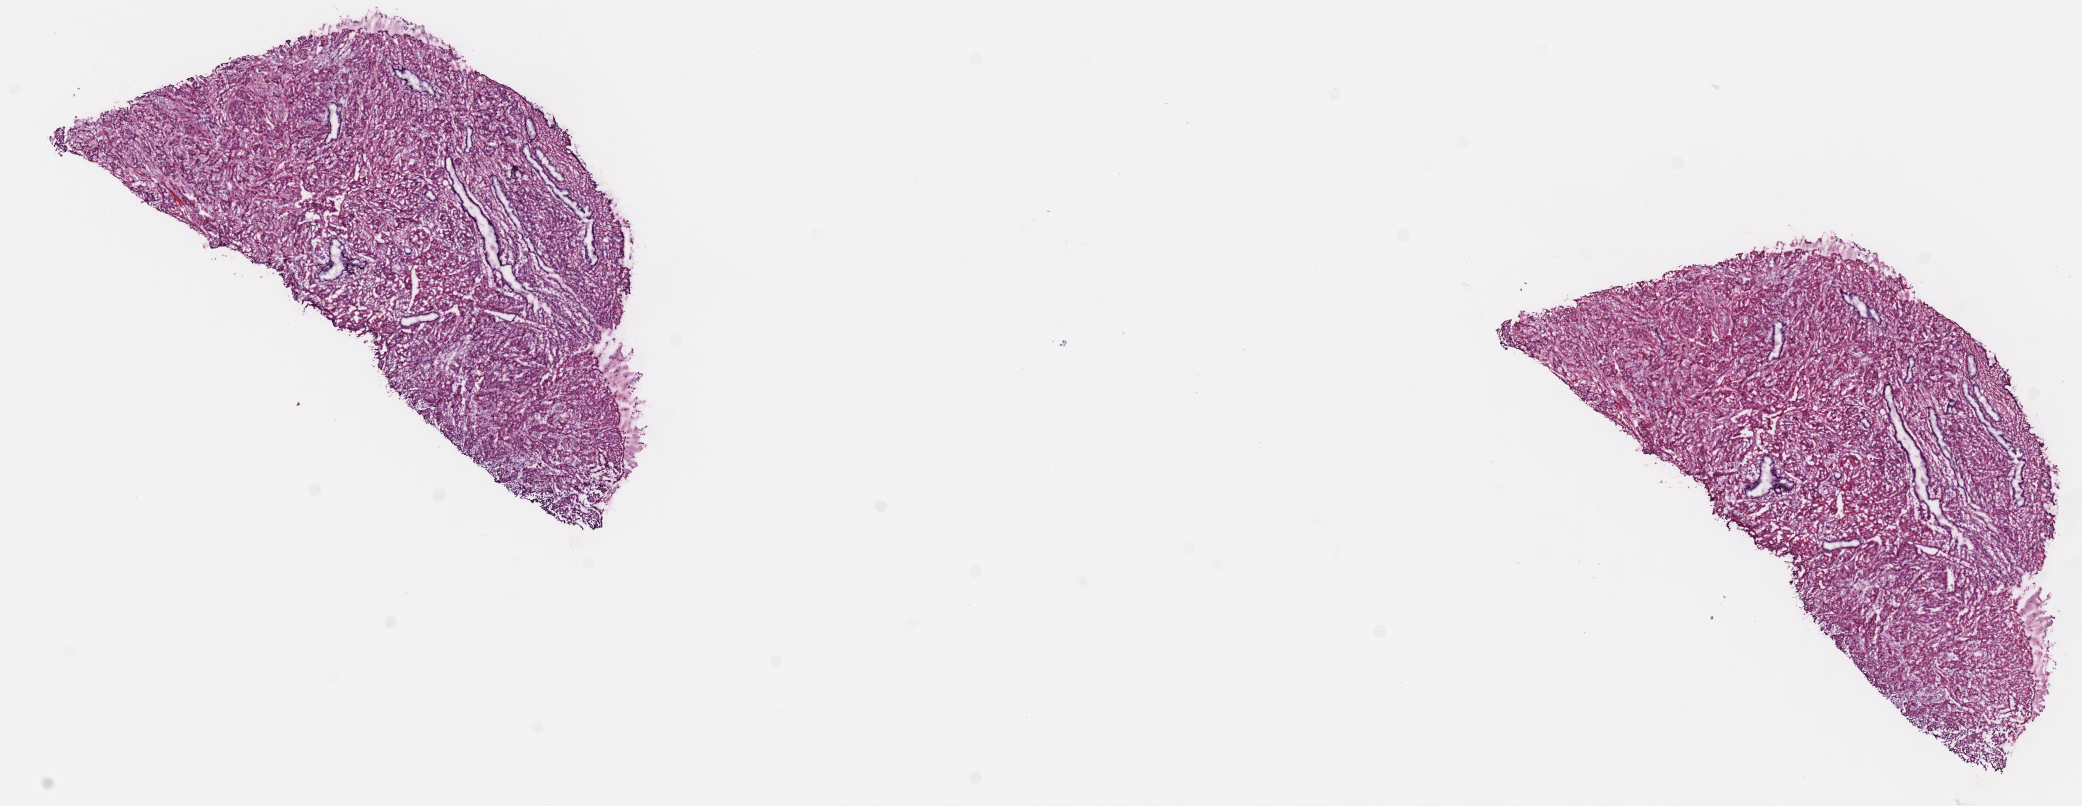
Whole-slide histology image, Hematoxylin and eosin (H&E) stained, a low-resolution overview of the entire scanned area, about 16.4 x 6.4 mm (acquisition: 40x scan). Frozen section. Cervix, primary tumour sample. Female patient; age at initial diagnosis 33 years. Histologic grade: G3 (poorly differentiated). Slide review estimates, as recorded: tumour cells 84%, tumour nuclei 92%, normal cells 5%, stromal cells 10%, necrosis 1%. Inflammatory infiltration, as recorded: lymphocyte infiltration 2%, monocyte infiltration 0%, neutrophil infiltration 0%.
FIGO stage: IB1. Diagnosis: Squamous cell carcinoma, NOS (cervix uteri).